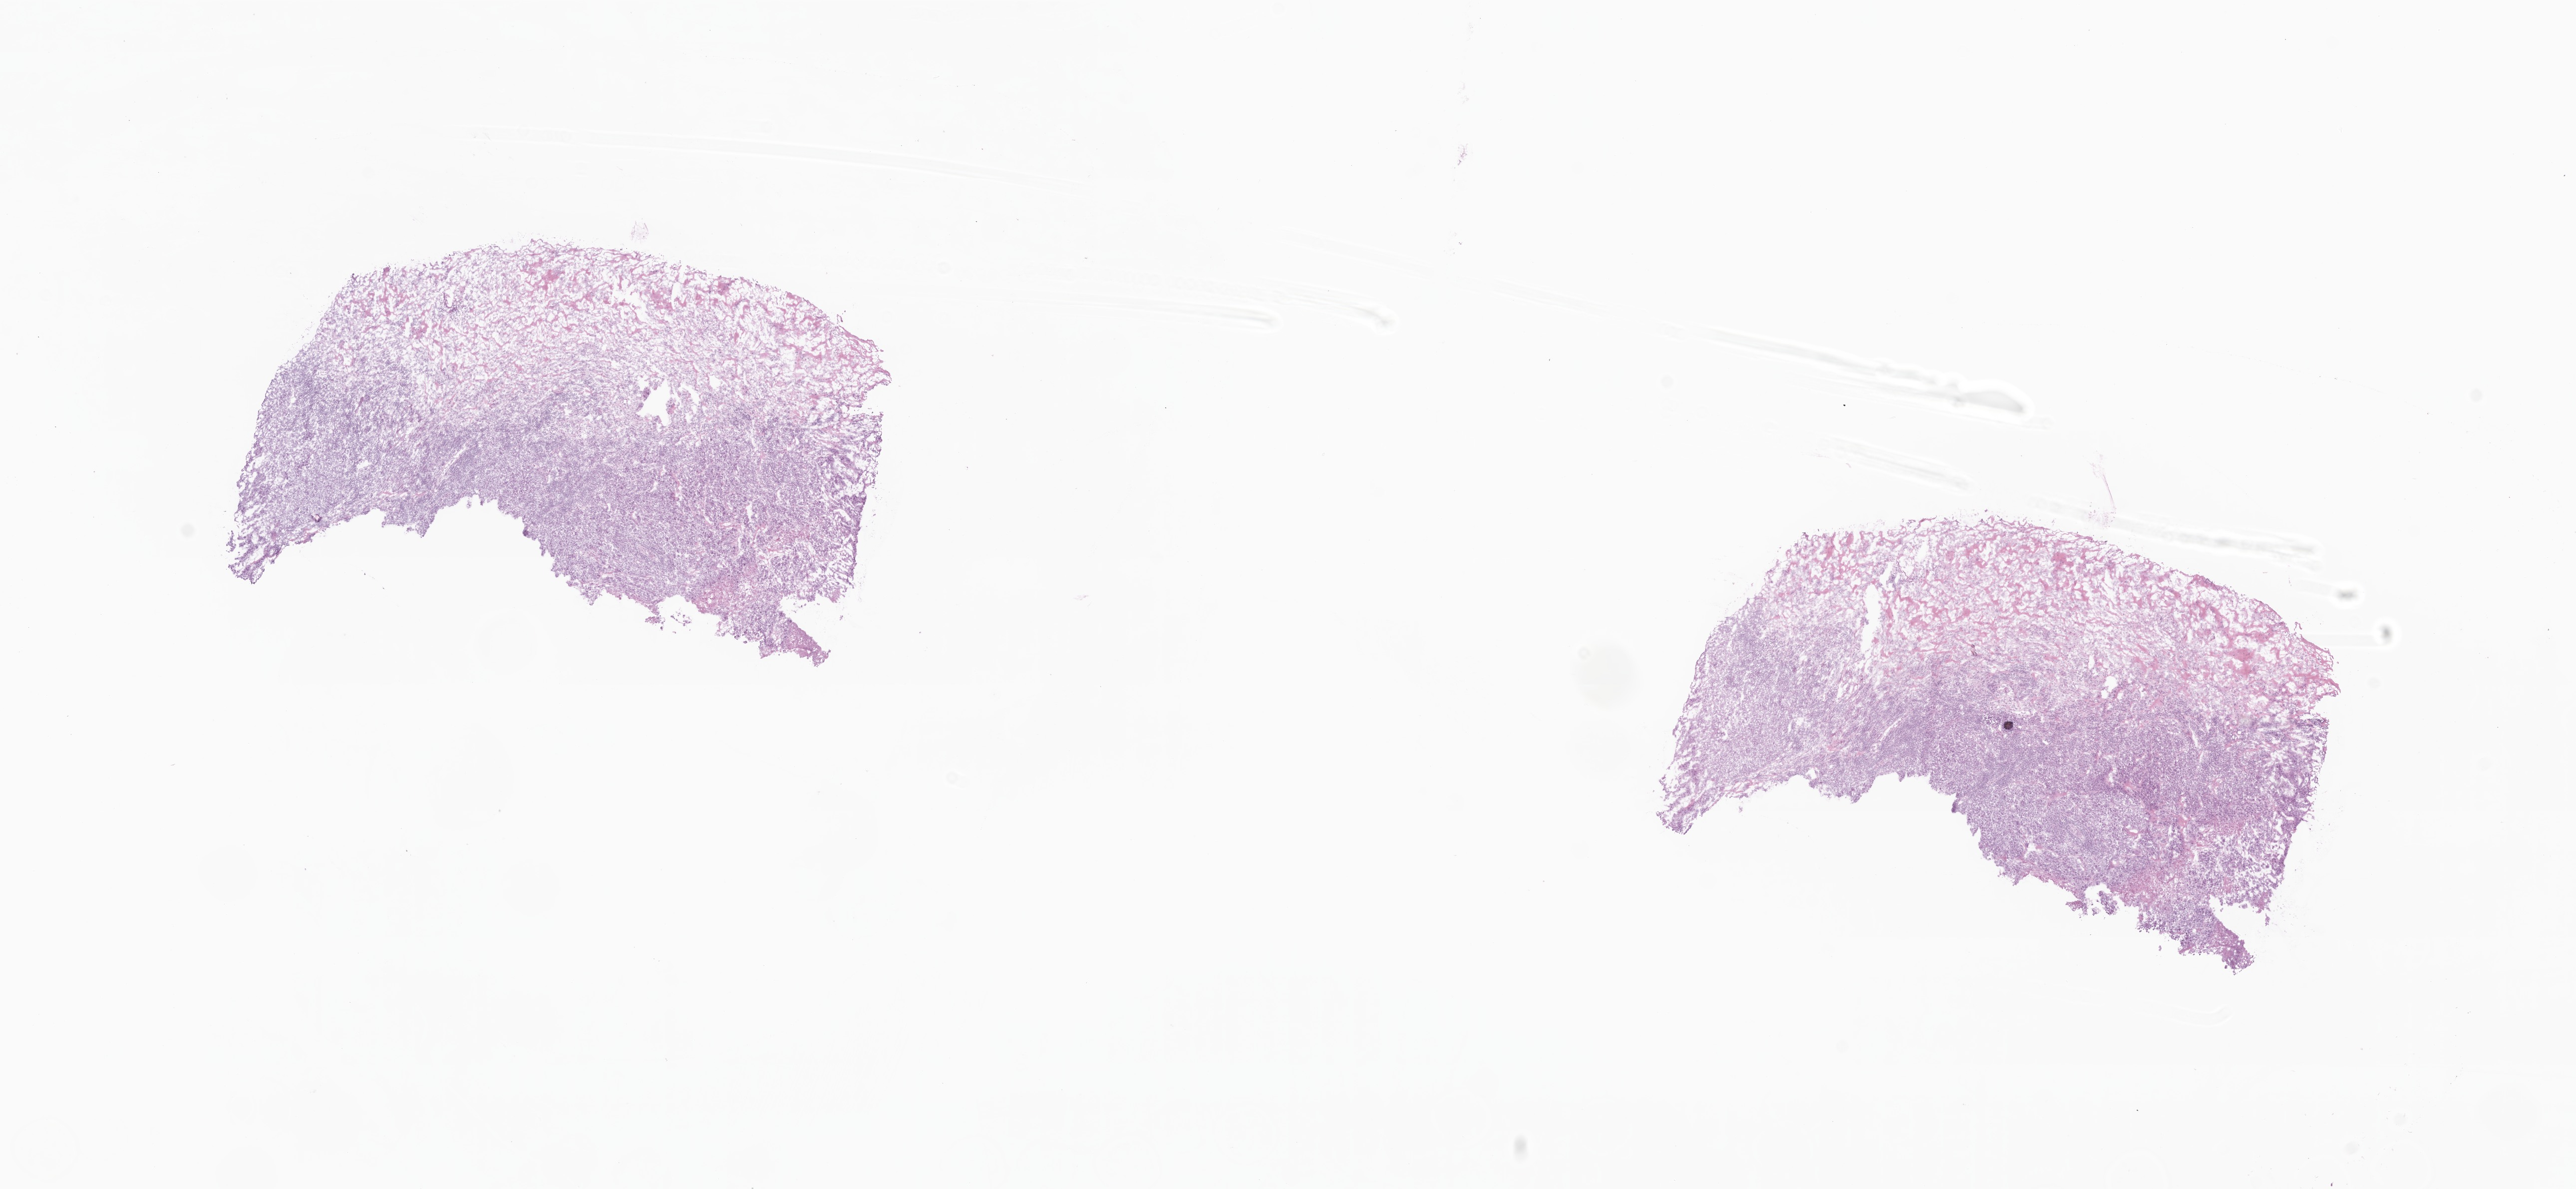
Whole-slide image, hematoxylin and eosin (H&E) stain — whole scanned area (about 21.8 x 10.0 mm) shown as a low-resolution overview. Frozen section. Specimen: metastatic tumor tissue, resected from lymph node. Male, age 66 years at initial diagnosis. Composition of this section per pathologist review: tumor cells 80%, tumor nuclei 80%, stromal cells 20%, necrosis 0%, normal cells 0%. Inflammatory infiltration, as recorded: lymphocyte infiltration 8%, monocyte infiltration 2%, neutrophil infiltration 6%.
* section: top of the tissue portion
* patient diagnosis (primary): Malignant melanoma, NOS